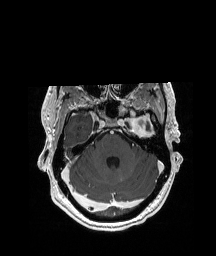
Brain MRI from a brain-tumour surgery series, one axial slice. T1-weighted post-contrast. 1 mm slice thickness. 216 × 256 image matrix, field of view 228 × 270 mm. Case-level facts recorded for this patient, not image findings: histopathology: Glioblastoma; WHO grade: 4; IDH mutation: no; tumour location: Left Anterior/Superior Temporal.
Structures marked on this image (expert manual segmentation):
- previous resection cavity: bounding box <146,123,152,132> (left, top, right, bottom; pixels)
- tumour: <123,108,158,134>